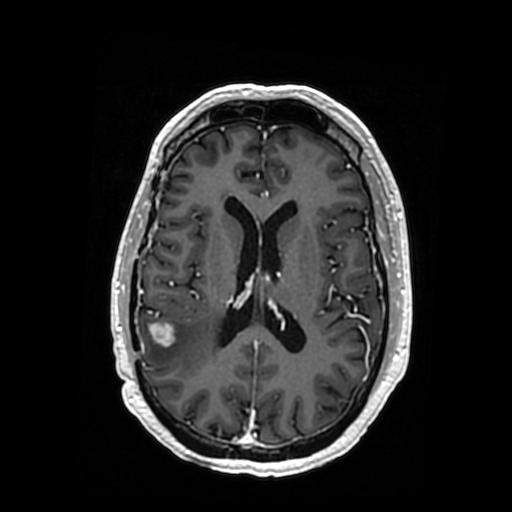
Brain MRI from a brain-tumour surgery series, one axial slice; slice 160 of 364 in the series (ordered by position); T1-weighted post-contrast; 0.5 mm slice thickness; 512 × 512 image matrix, field of view 260 × 260 mm. Case-level facts recorded for this patient, not image findings: histopathology: Oligodendroglioma; WHO grade: 3; IDH mutation: yes; tumour location: Right Posterior Temporal Inferior Parietal.
Outlined on this slice (manually delineated by an expert):
- tumour: bounding box (x1, y1, x2, y2) in pixels: (146, 321, 217, 346)